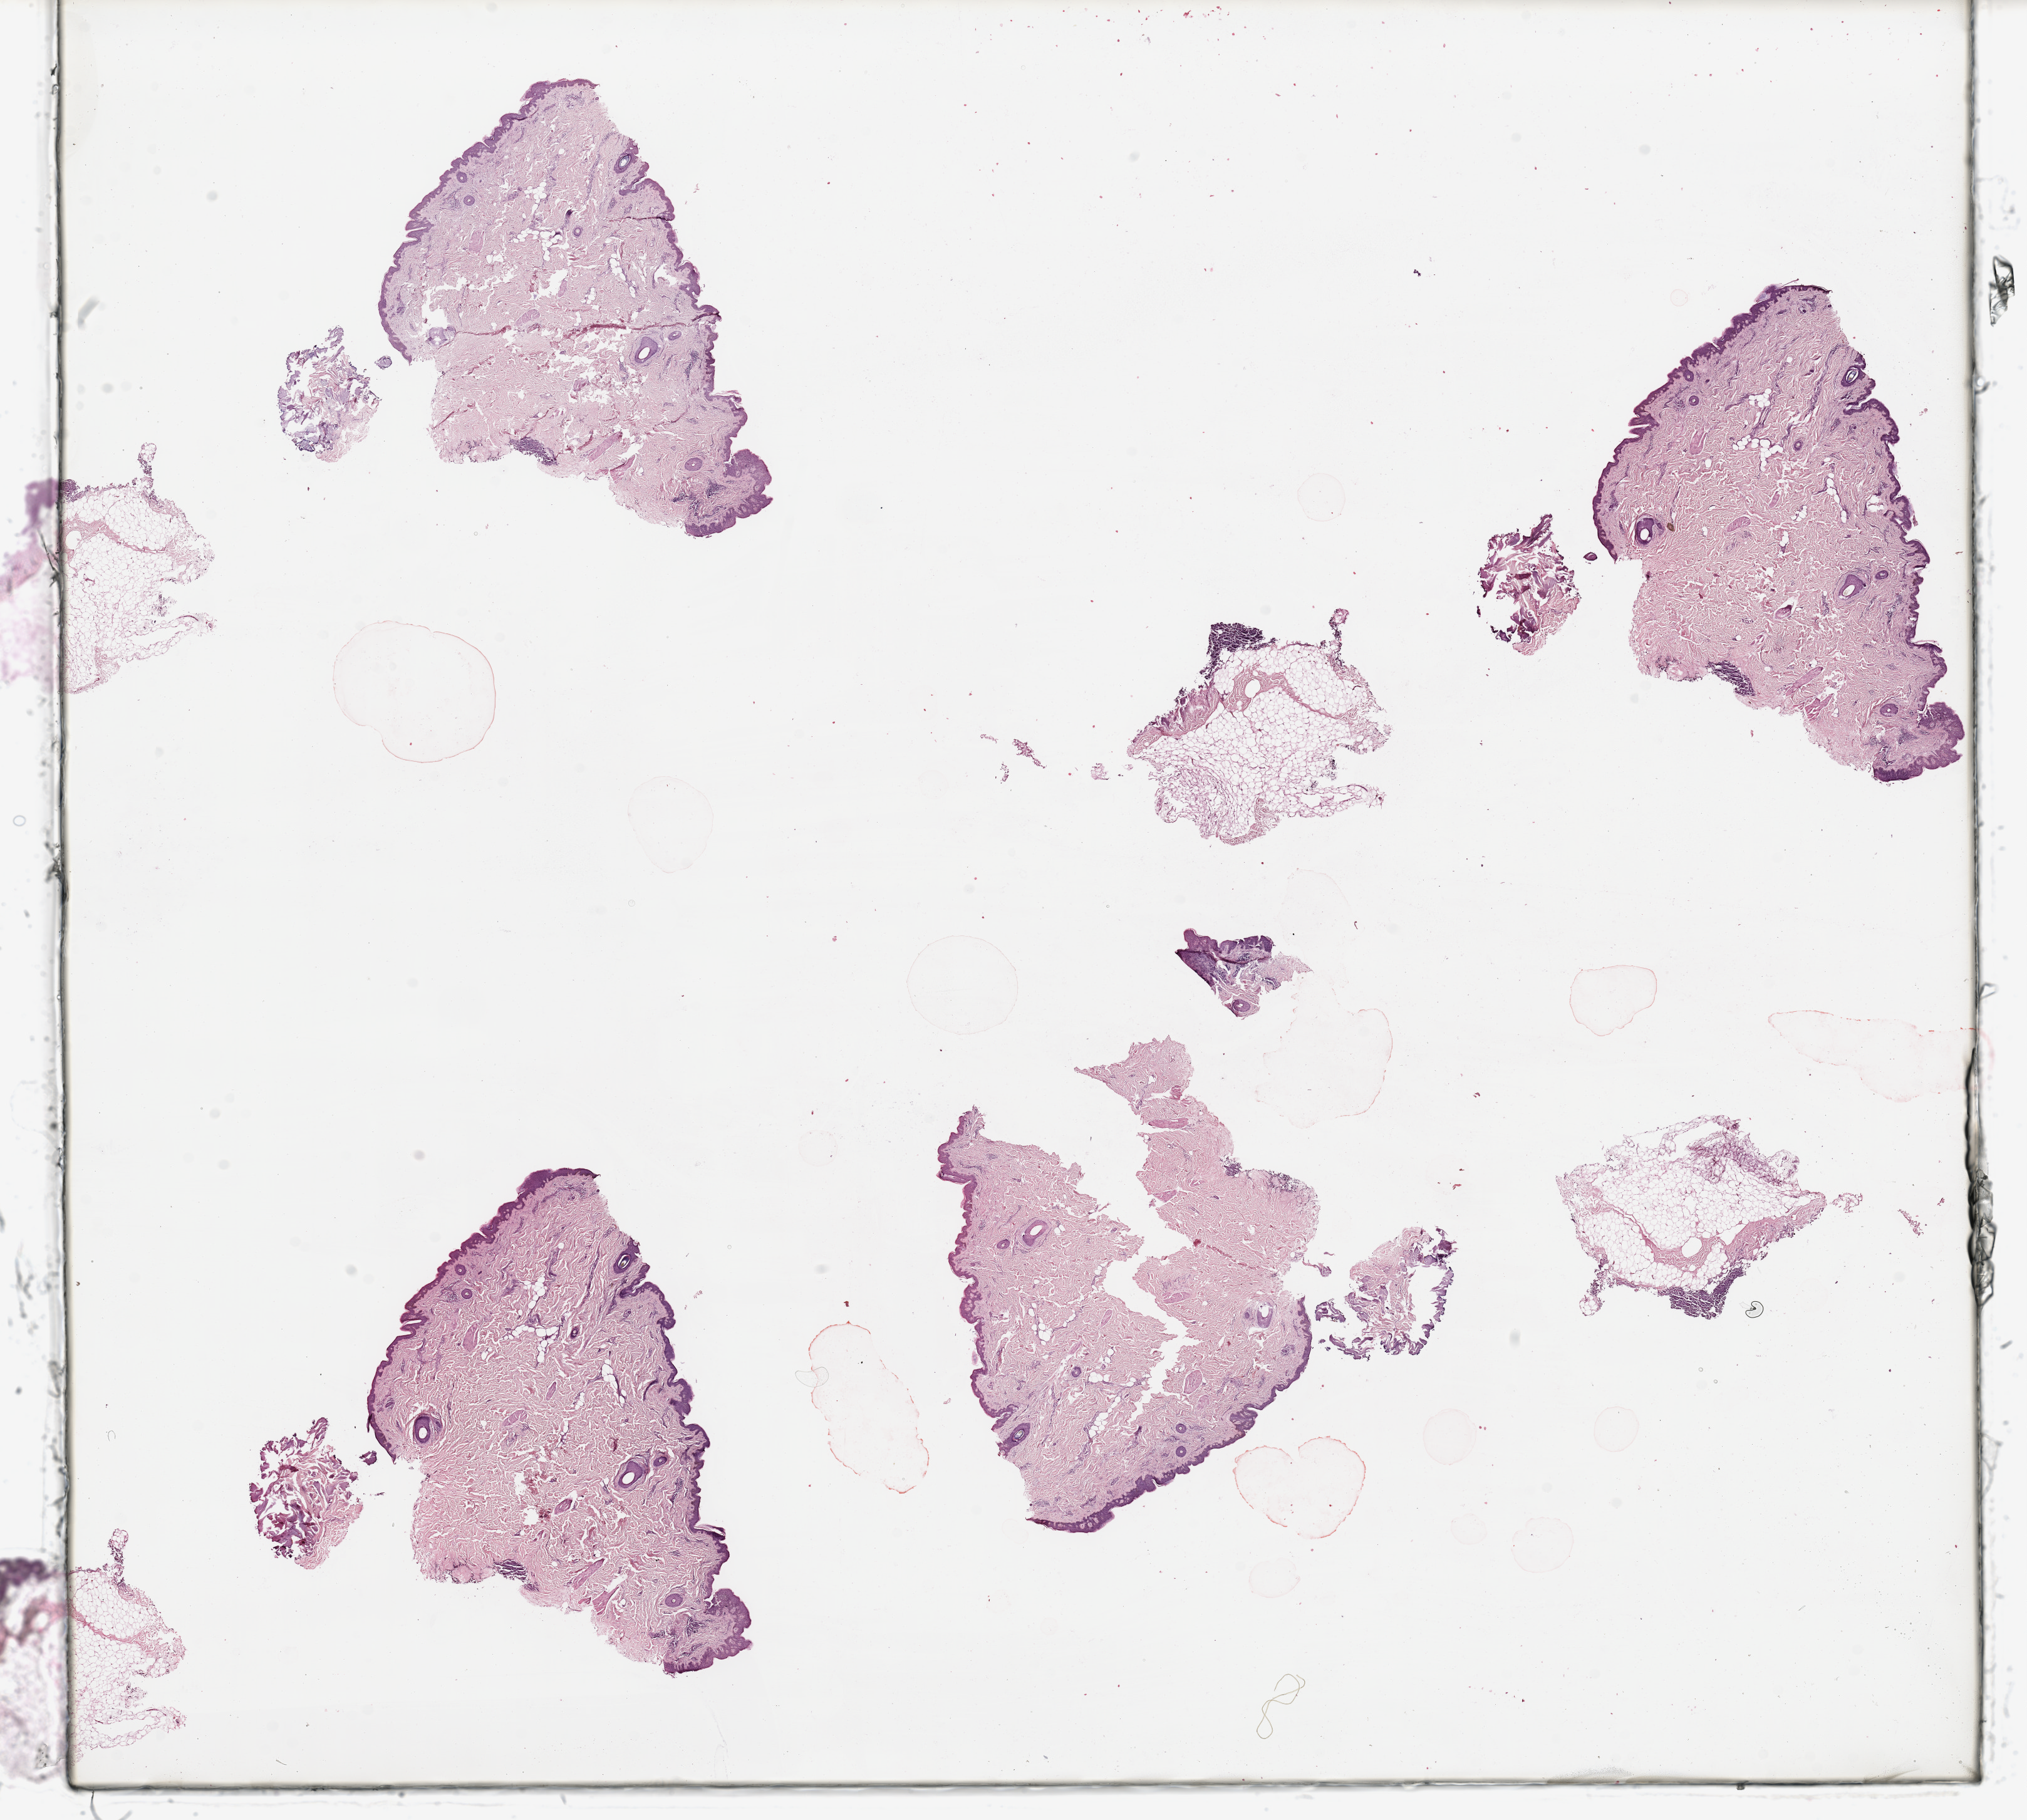
Whole-slide histology image, H&E-stained, low-resolution overview of the scanned area, about 25.6 x 23.0 mm (from a 20x scan). Normal (non-tumour) tissue (melanoma cohort); sampled site not recorded. 60-year-old male patient.
This section: normal (non-tumour) tissue from the same patient. Patient diagnosis: Malignant melanoma, NOS.